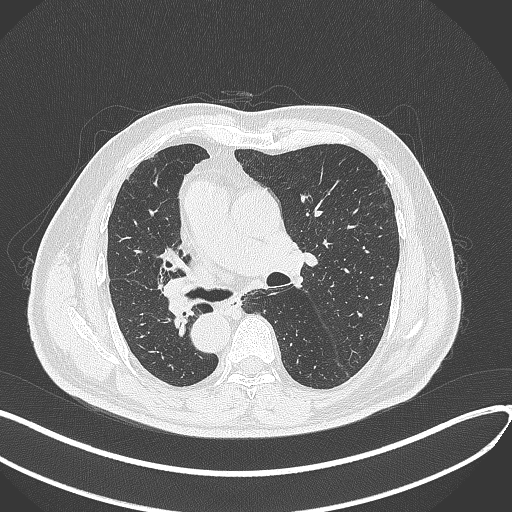
Chest CT, one axial slice; position 161 of 300 along the scan axis; reconstruction kernel B70f; 120 kVp; lung window (W 1500 / L -600 HU); 1 mm slice thickness; 512 × 512 image matrix, field of view 400 × 400 mm. Patient: male, 67 years. From the clinical record (not read from this slice): clinical TNM (as recorded): T2a N0 M0.
Annotated regions visible in this slice (bounding box drawn by a radiologist):
- lung tumour (recorded histology: squamous cell carcinoma): bounding box (x1, y1, x2, y2) in pixels: (160, 274, 199, 323)